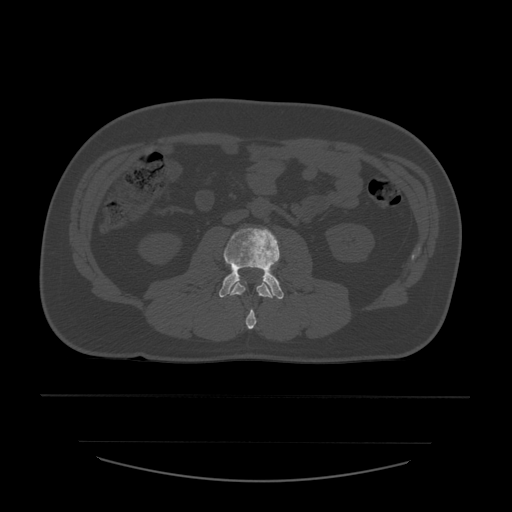
CT including the spine, one axial slice. Position 183 of 532 along the scan axis. 120 kVp. Bone window (W 1800 / L 400 HU). 512 × 512 image matrix. Patient age 44 years. From the clinical record (not read from this slice): primary cancer: soft tissue sarcoma.
Structures marked on this image (semi-automatically segmented with operator editing):
- L2 vertebra: bounding box [x1, y1, x2, y2] px = [230, 282, 274, 330]
- L3 vertebra: [219, 228, 284, 300]